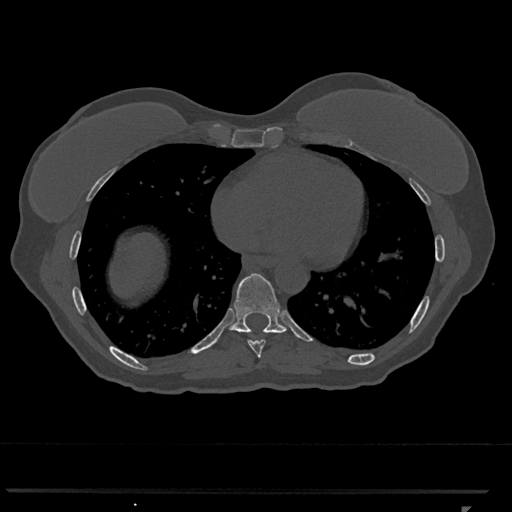
CT including the spine, one axial slice; slice 637 of 793 in the series (ordered by position); reconstruction kernel Br40s/3; bone window (W 1800 / L 400 HU); 0.5 mm slice thickness; 512 × 512 image matrix. Female patient, age 62 years. From the clinical record (not read from this slice): primary cancer: renal.
Annotated regions visible in this slice (semi-automatically segmented with operator editing):
- T8 vertebra: bounding box <248,339,266,358> (left, top, right, bottom; pixels)
- T9 vertebra: <229,273,287,333>